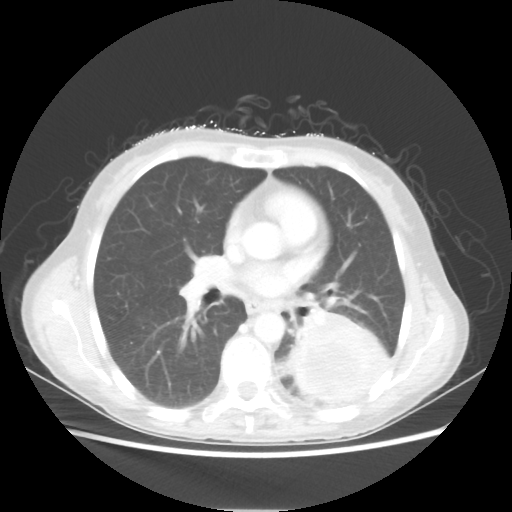
Chest CT, one axial slice. Slice 30 of 56 in the series (ordered by position). 80 kVp. Lung window (W 1500 / L -600 HU). 512 × 512 image matrix, field of view 360 × 360 mm. Patient: female, 53 years. Case-level facts recorded for this patient, not image findings: clinical TNM (as recorded): T3 N0 M0.
Annotated regions visible in this slice (bounding box drawn by a radiologist):
- lung tumour (recorded histology: adenocarcinoma): bounding box <287,309,390,405> (left, top, right, bottom; pixels)